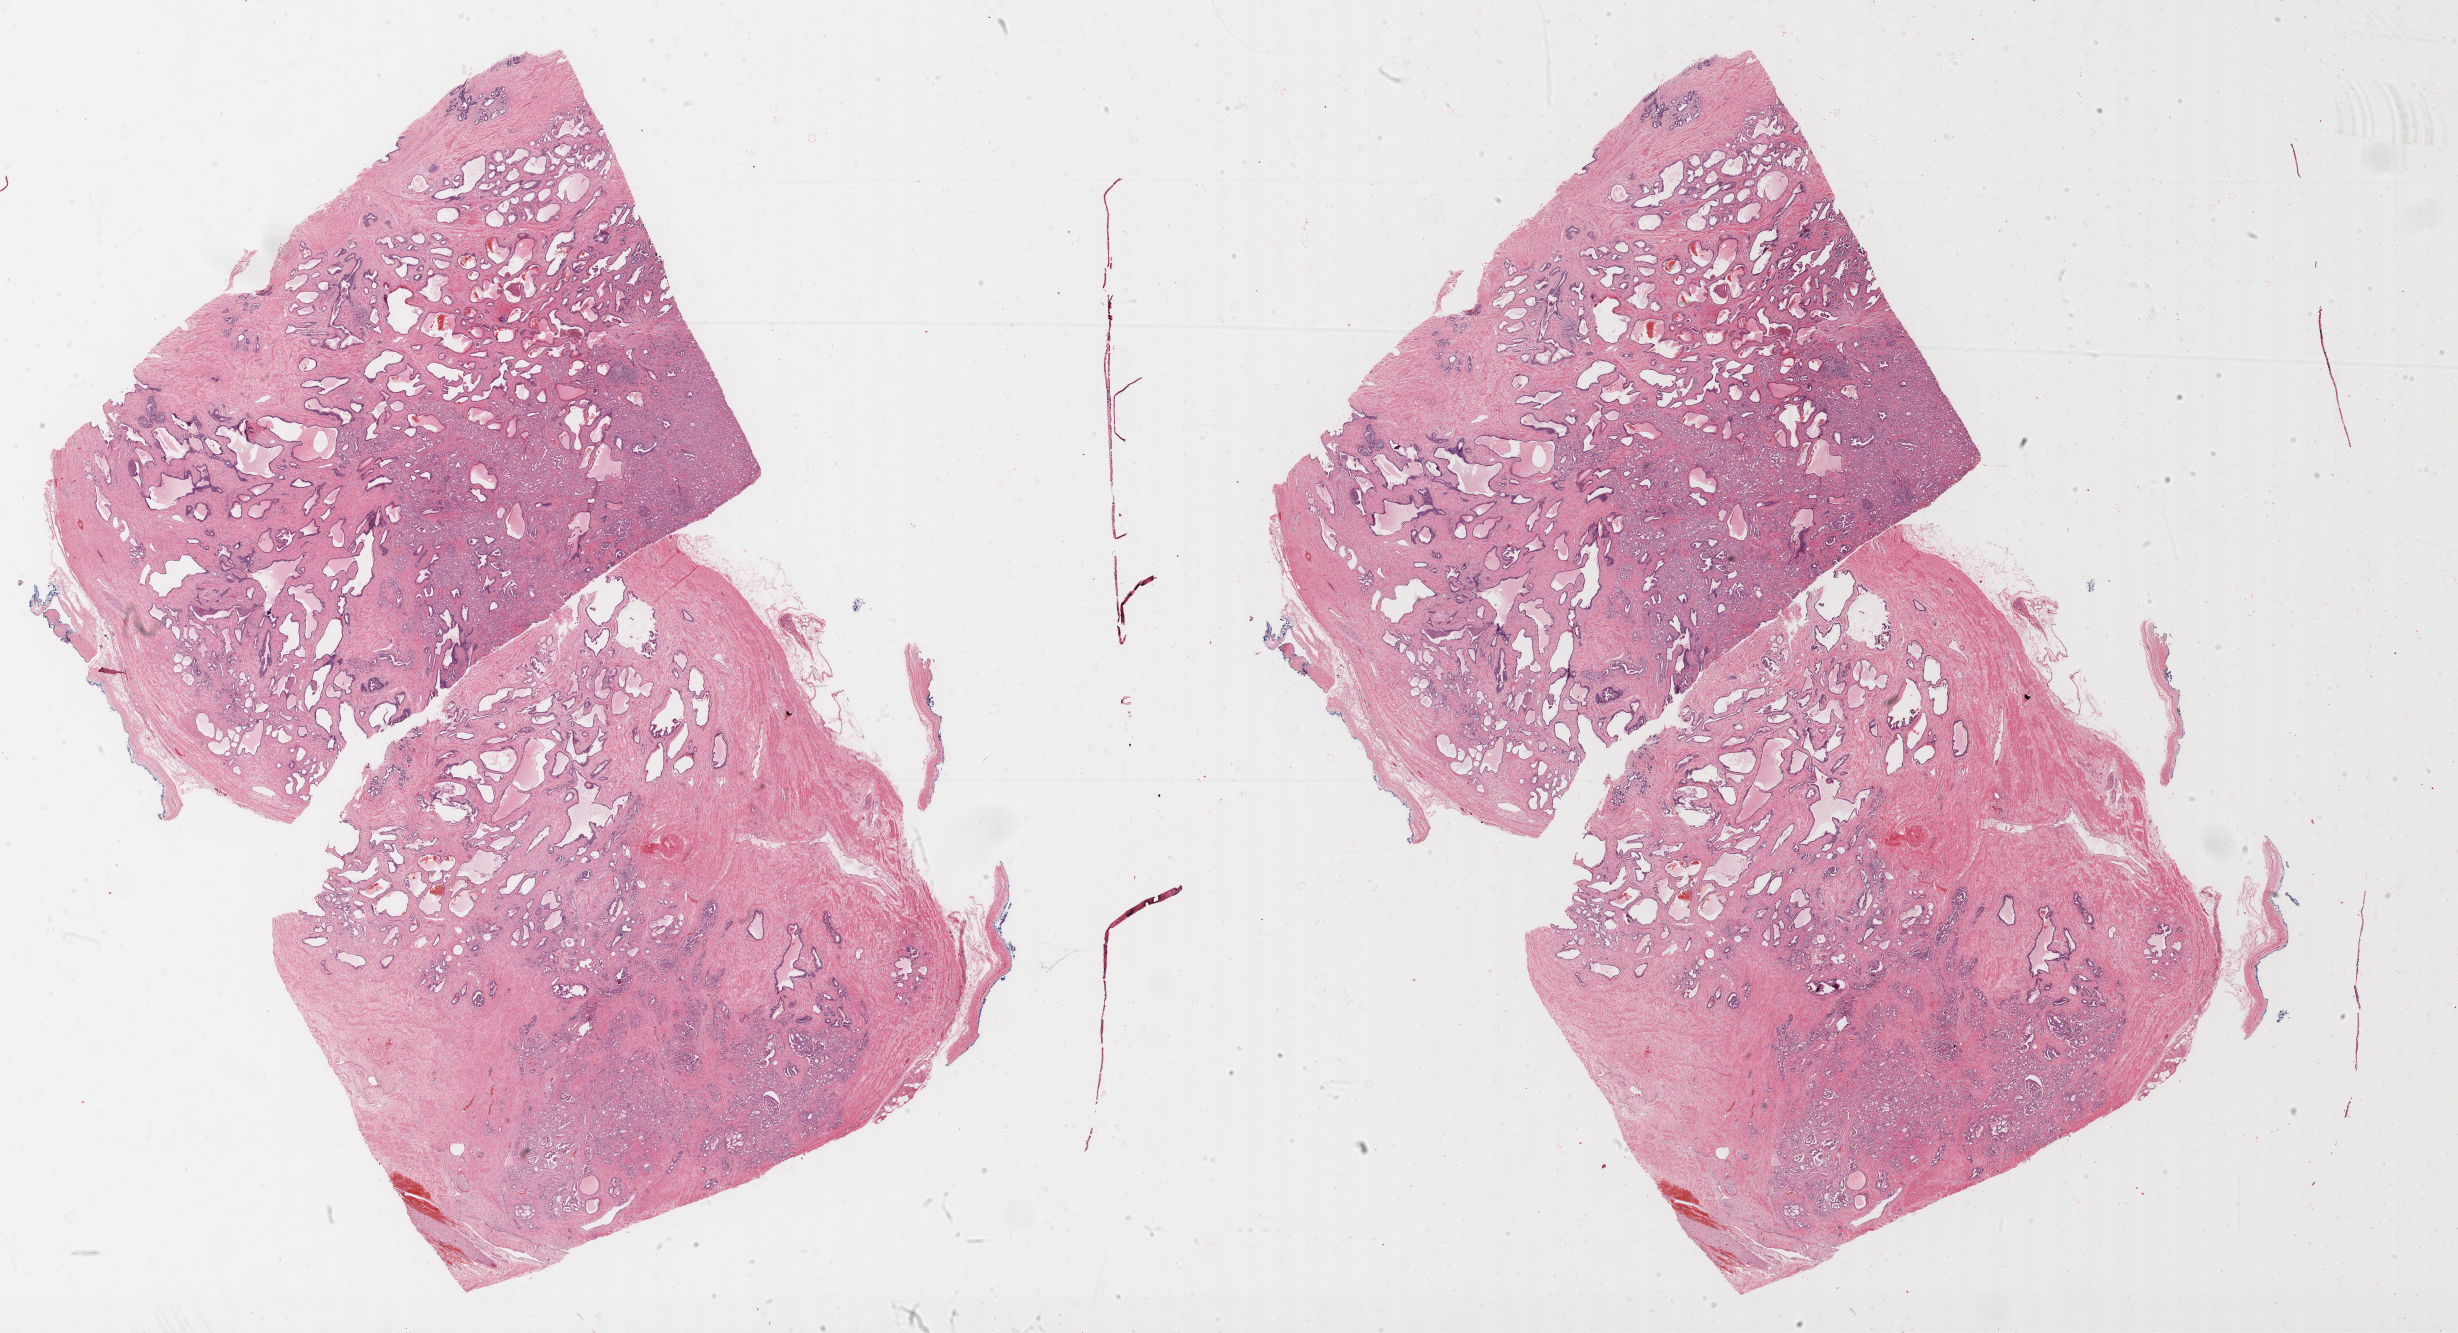
Whole-slide histology image, Hematoxylin and eosin (H&E) stained, low-resolution overview of the scanned area, about 39.8 x 21.6 mm (acquisition: 40x scan); formalin-fixed paraffin-embedded (FFPE) diagnostic section; prostate, primary tumour sample. Patient: male, age at initial diagnosis 63 years.
Pathologic diagnosis: Adenocarcinoma, NOS (prostate gland).